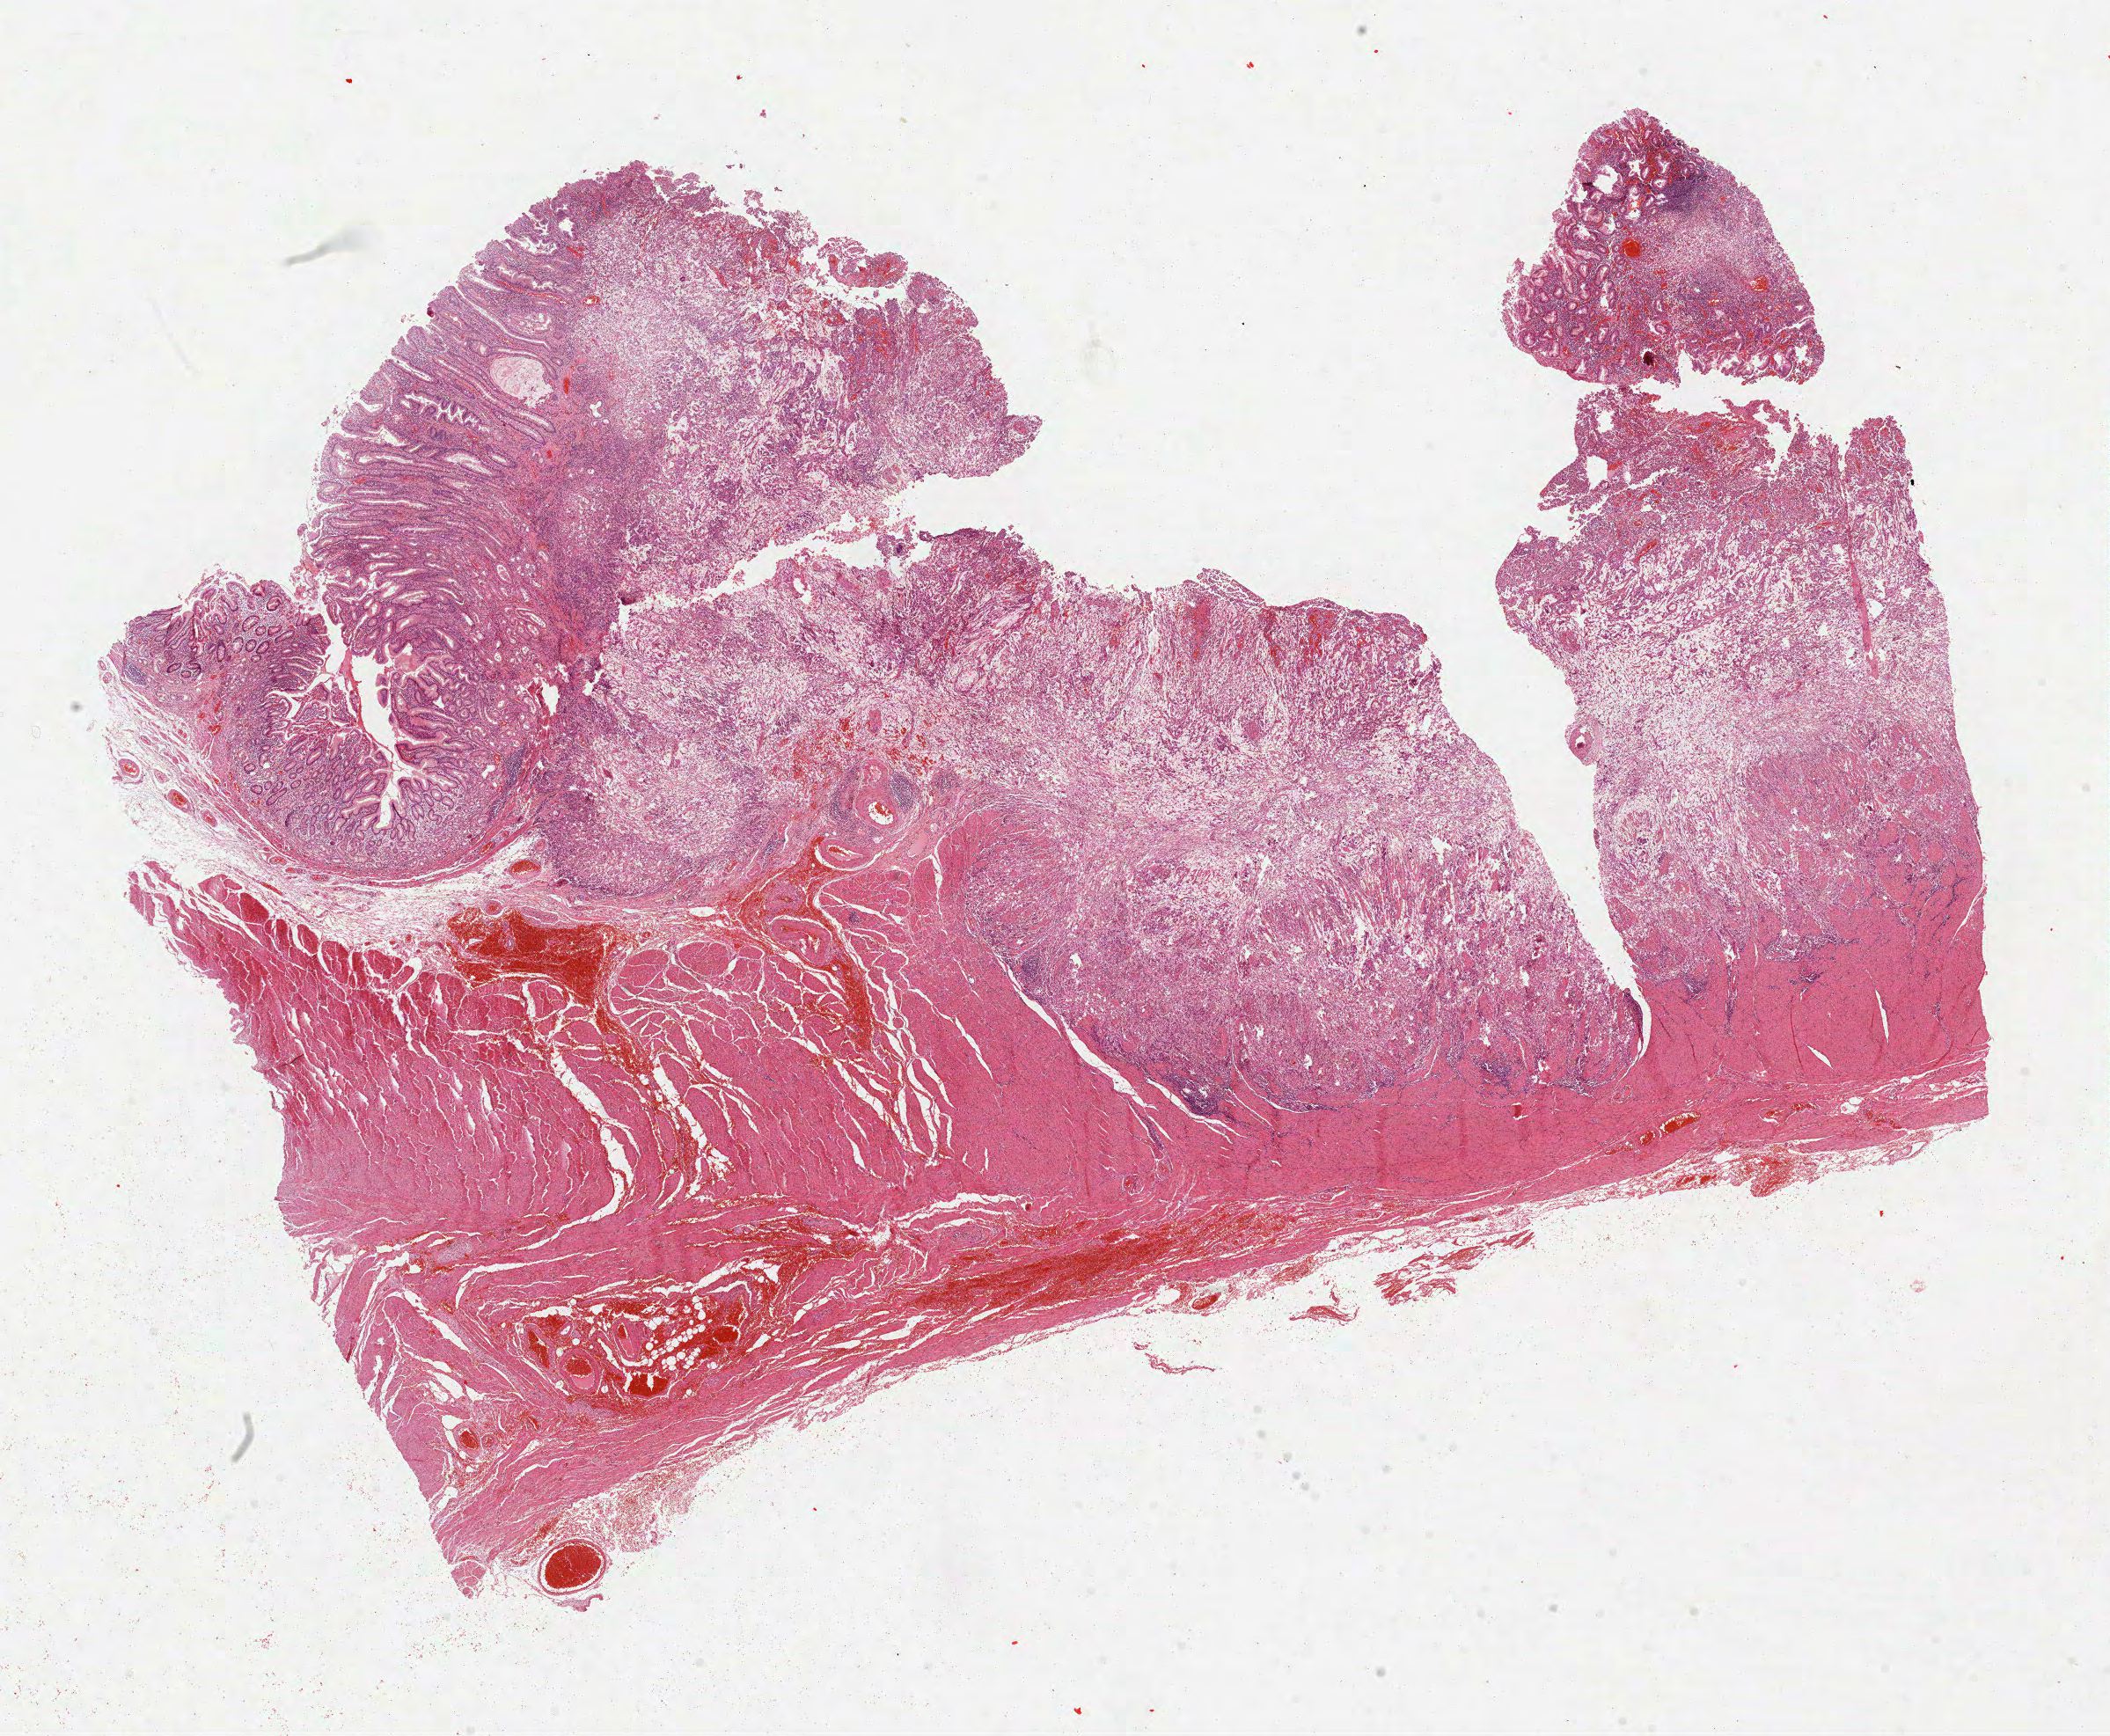
Whole-slide histology image, H&E-stained, shown as a low-resolution overview of the whole scanned area (about 19.3 x 15.9 mm, from a 40x scan). Formalin-fixed paraffin-embedded (FFPE) diagnostic section. Sample: primary tumour, stomach. Male patient; age at initial diagnosis 58 years. Histologic grade: G3 (poorly differentiated).
• AJCC pathologic stage: IB
• lymph nodes positive (case pathology): 0 of 11 examined
• diagnosis: Carcinoma, diffuse type